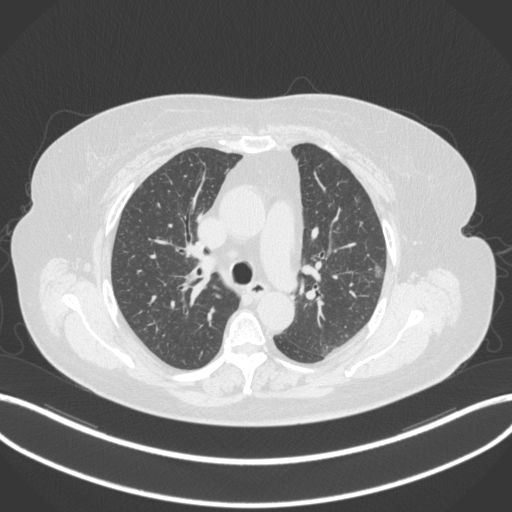
Chest CT, one axial slice; slice 213 of 310 in the series (ordered by position); reconstruction kernel B31f; 120 kVp; lung window (W 1500 / L -600 HU); 1 mm slice thickness; 512 × 512 image matrix. Female patient, age 70 years. From the clinical record (not read from this slice): clinical TNM (as recorded): T1c N0 M0.
Structures marked on this image (bounding box drawn by a radiologist):
- lung tumour (recorded histology: adenocarcinoma): bounding box <374,261,384,285> (left, top, right, bottom; pixels)